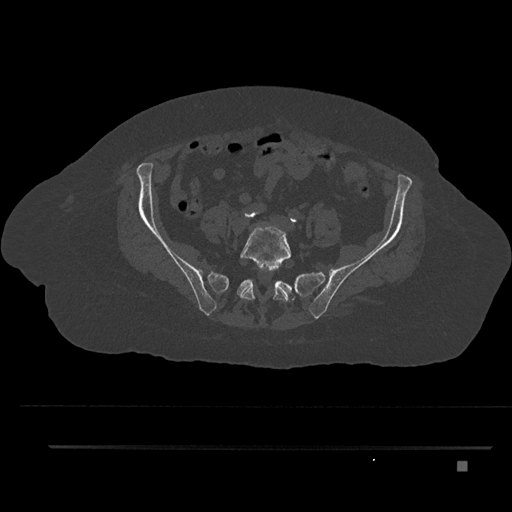
CT including the spine, one axial slice. Position 27 of 797 along the scan axis. Bone window (W 1800 / L 400 HU). 0.5 mm slice thickness. 512 × 512 image matrix, field of view 437 × 437 mm. Female patient, age 76 years. From the clinical record (not read from this slice): primary cancer: lung; vertebrae with lytic lesions (as recorded): T11, L3.
Outlined on this slice (semi-automatically segmented with operator editing):
- L5 vertebra: bounding box [x1, y1, x2, y2] px = [240, 224, 292, 318]